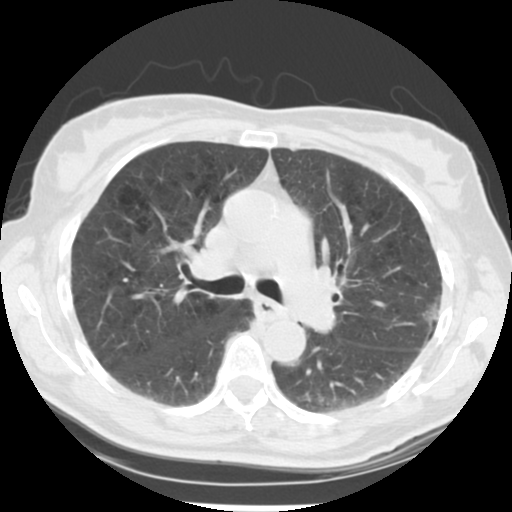
Low-dose screening chest CT, one axial slice. Slice 137 of 223 in the series (ordered by position). Reconstruction kernel STANDARD. Lung window (W 1500 / L -600 HU). 2.5 mm slice thickness. 512 × 512 image matrix.
Structures marked on this image (expert manual segmentation):
- lesion 1 (tumor, upper lobe of left lung): box from (x=423, y=296) to (x=440, y=326) px